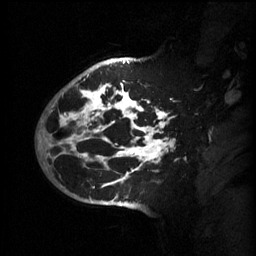
Breast MRI (dynamic contrast-enhanced), one sagittal slice; position 43 of 60 along the scan axis; 3 images stored at this slice position (order not interpretable as contrast timing); 1.5 T; TE 4.2 ms, TR 11 ms; 2 mm slice thickness; 256 × 256 image matrix, field of view 220 × 220 mm. Female patient, age 51 years.
Annotated regions visible in this slice (semi-automatically segmented with operator editing):
- analysis volume of interest (the breast-tissue region the enhancement analysis was run in; not a lesion): bounding box (x1, y1, x2, y2) in pixels: (63, 80, 175, 201)
- tumour enhancement mask (voxels above the 70 % enhancement threshold inside the analysis volume of interest): (63, 84, 175, 189)